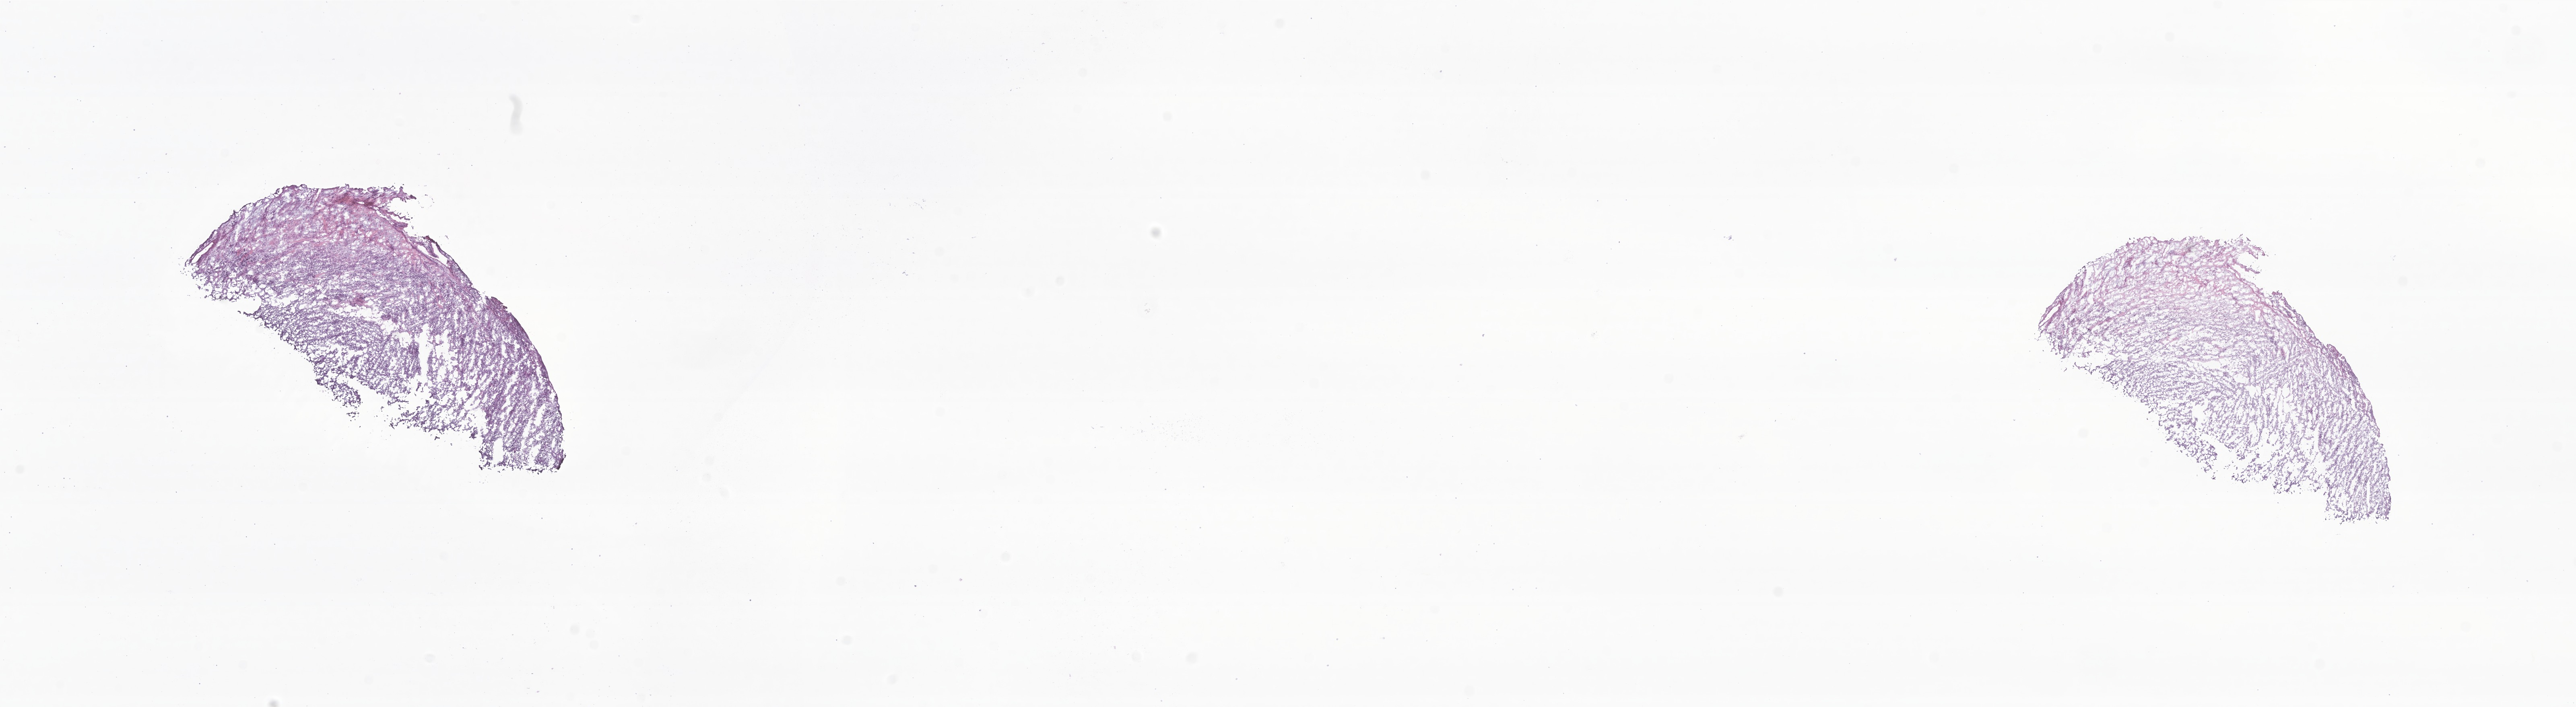
Digitized haematoxylin and eosin-stained section of tumor tissue from the retroperitoneum — low-resolution overview of the scanned area, about 27.0 x 7.4 mm. Cryosection (OCT / tissue freezing medium). Patient: female, age 76 months (6 years 4 months).
Diagnosis: Sarcoma, NOS.